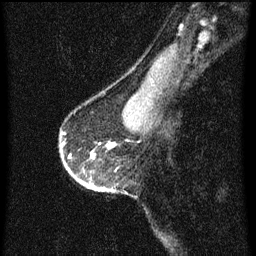
Breast MRI (dynamic contrast-enhanced), one sagittal slice. Position 49 of 60 along the scan axis. Dynamic contrast-enhanced series, image 2 of 3 at this slice position (ordered by acquisition). 1.5 T. TE 4.2 ms, TR 8 ms. 256 × 256 image matrix, field of view 180 × 180 mm. Patient: female, 56 years.
Annotated regions visible in this slice (semi-automatically segmented with operator editing):
- analysis volume of interest (the breast-tissue region the enhancement analysis was run in; not a lesion): bounding box [x1, y1, x2, y2] px = [59, 130, 120, 193]
- tumour enhancement mask (voxels above the 70 % enhancement threshold inside the analysis volume of interest): [98, 188, 105, 191]